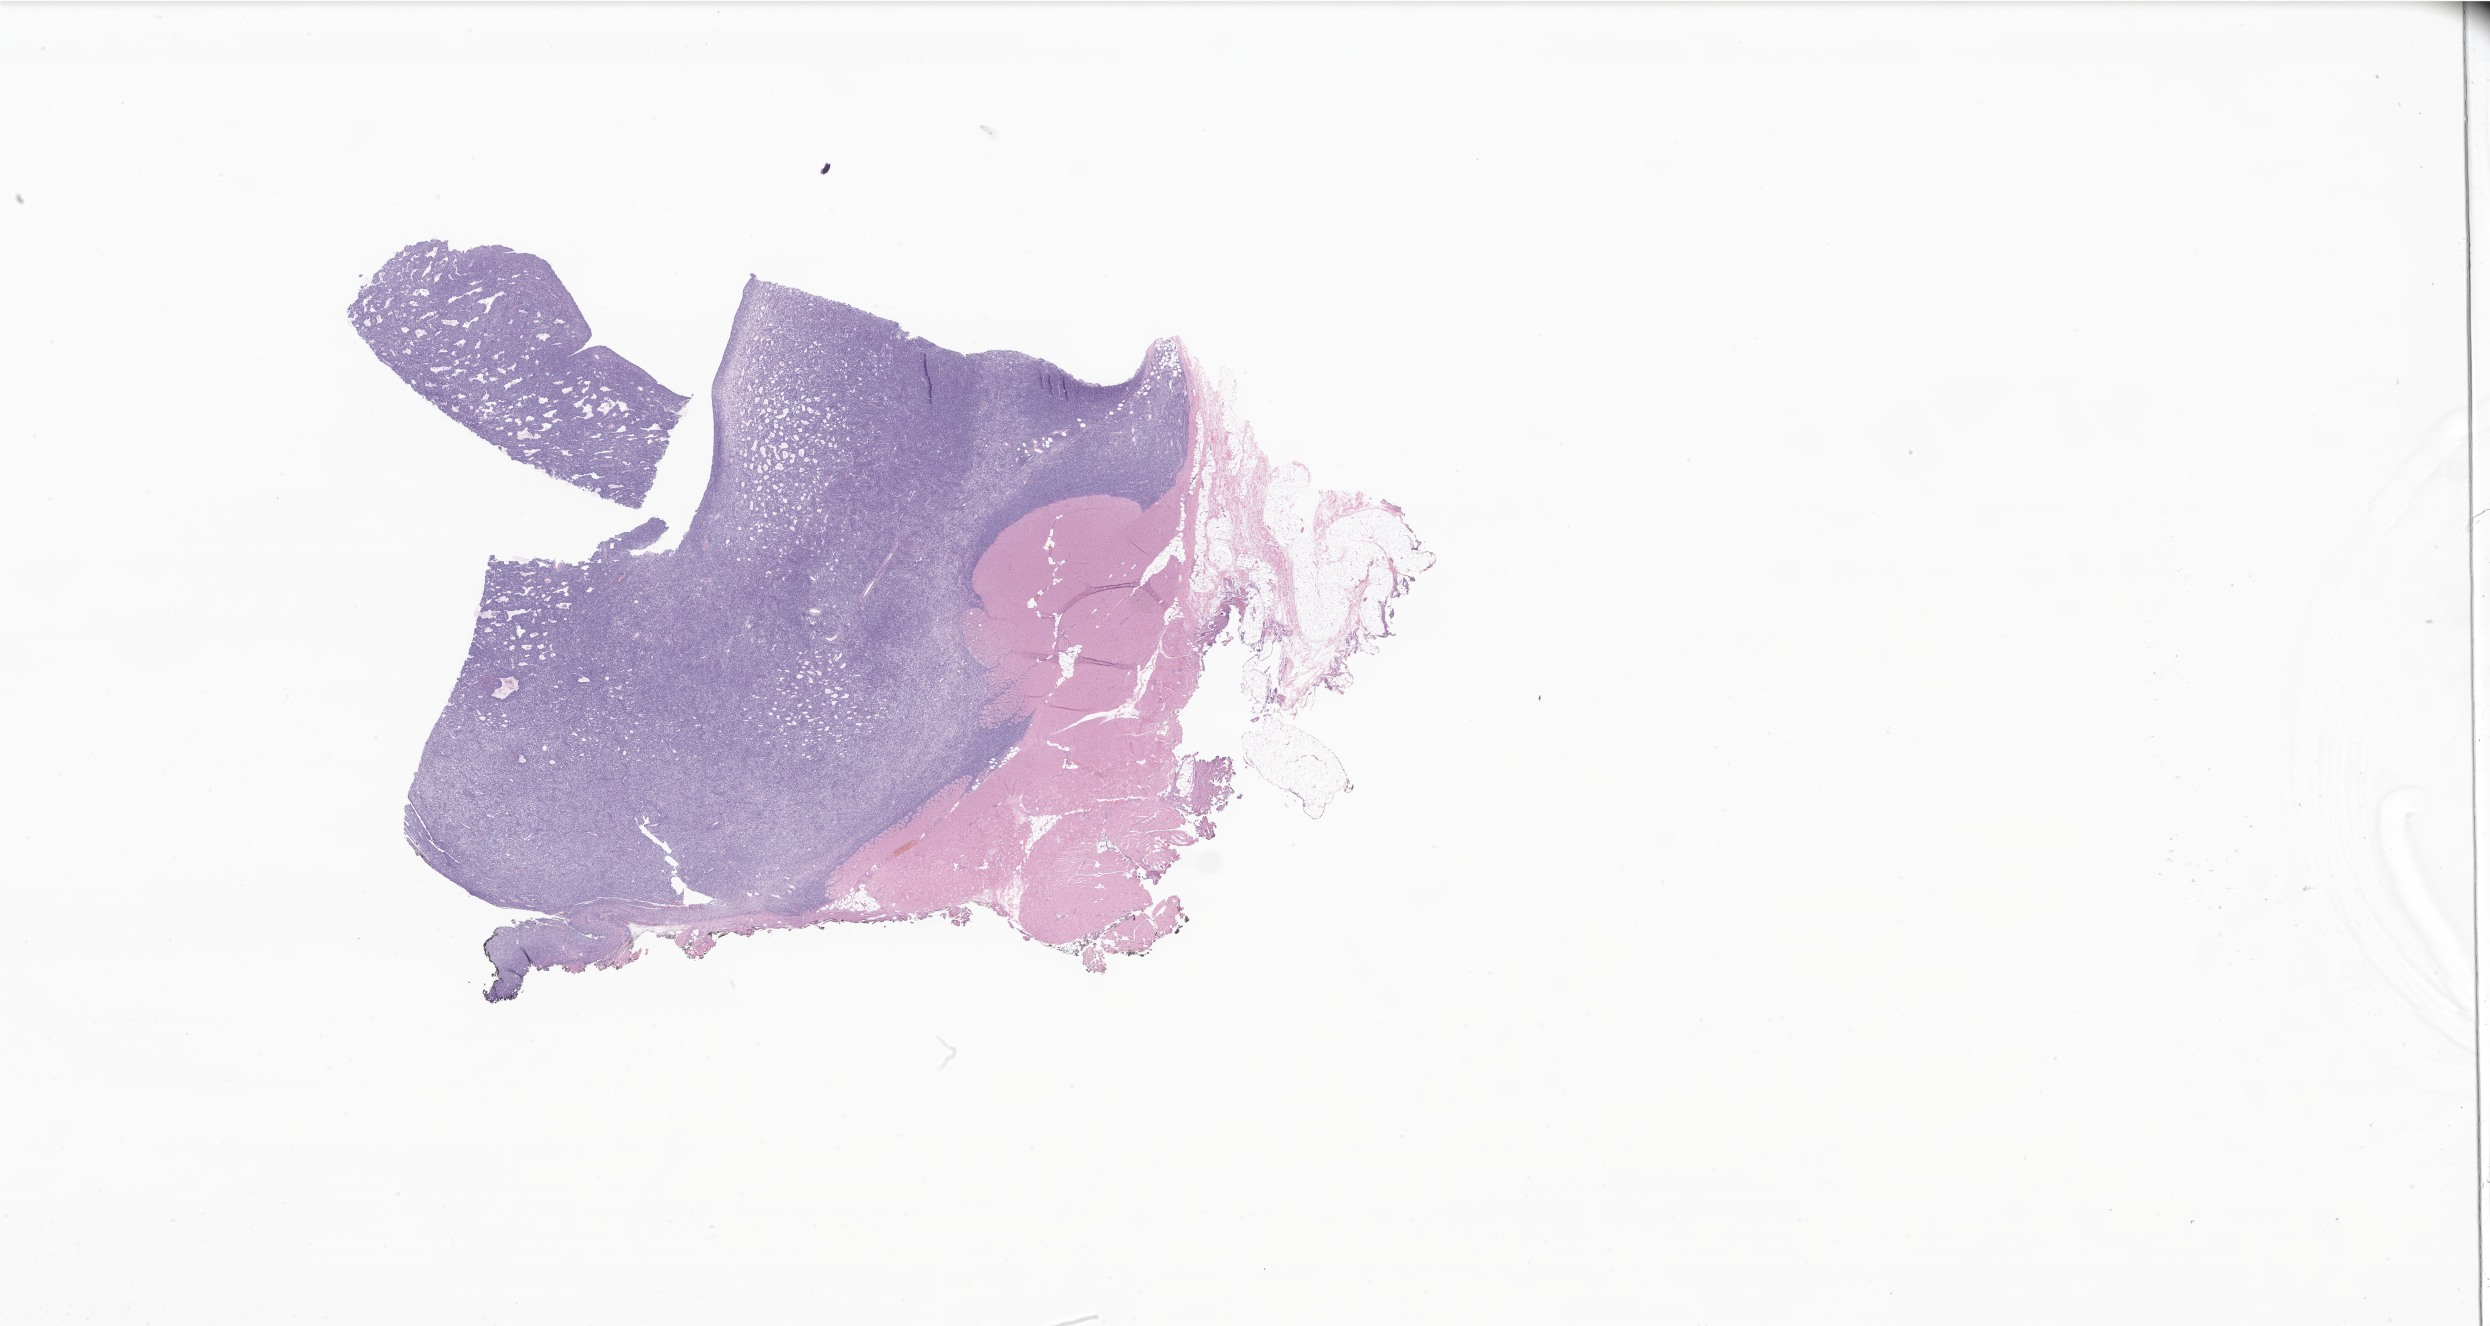
Digitized hematoxylin and eosin (H&E)-stained section of tumor tissue from the soft tissue, shown as a low-resolution overview of the whole scanned area (about 42.0 x 22.4 mm), formalin-fixed paraffin-embedded section. Patient: male, age 95 months.
Diagnosis (ICD-O-3 morphology term): Alveolar rhabdomyosarcoma.